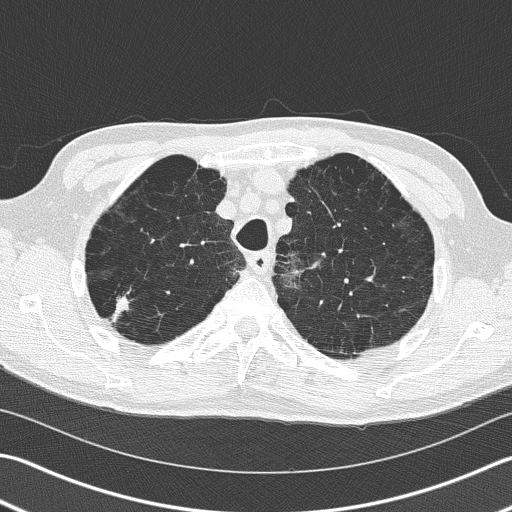
Low-dose screening chest CT, one axial slice; position 126 of 163 along the scan axis; reconstruction kernel B50f; 120 kVp; lung window (W 1500 / L -600 HU); 2 mm slice thickness; 512 × 512 image matrix.
Outlined on this slice (outlined manually by an expert reader):
- lesion 1 (tumor, upper lobe of right lung): bounding box (x1, y1, x2, y2) in pixels: (114, 296, 129, 319)